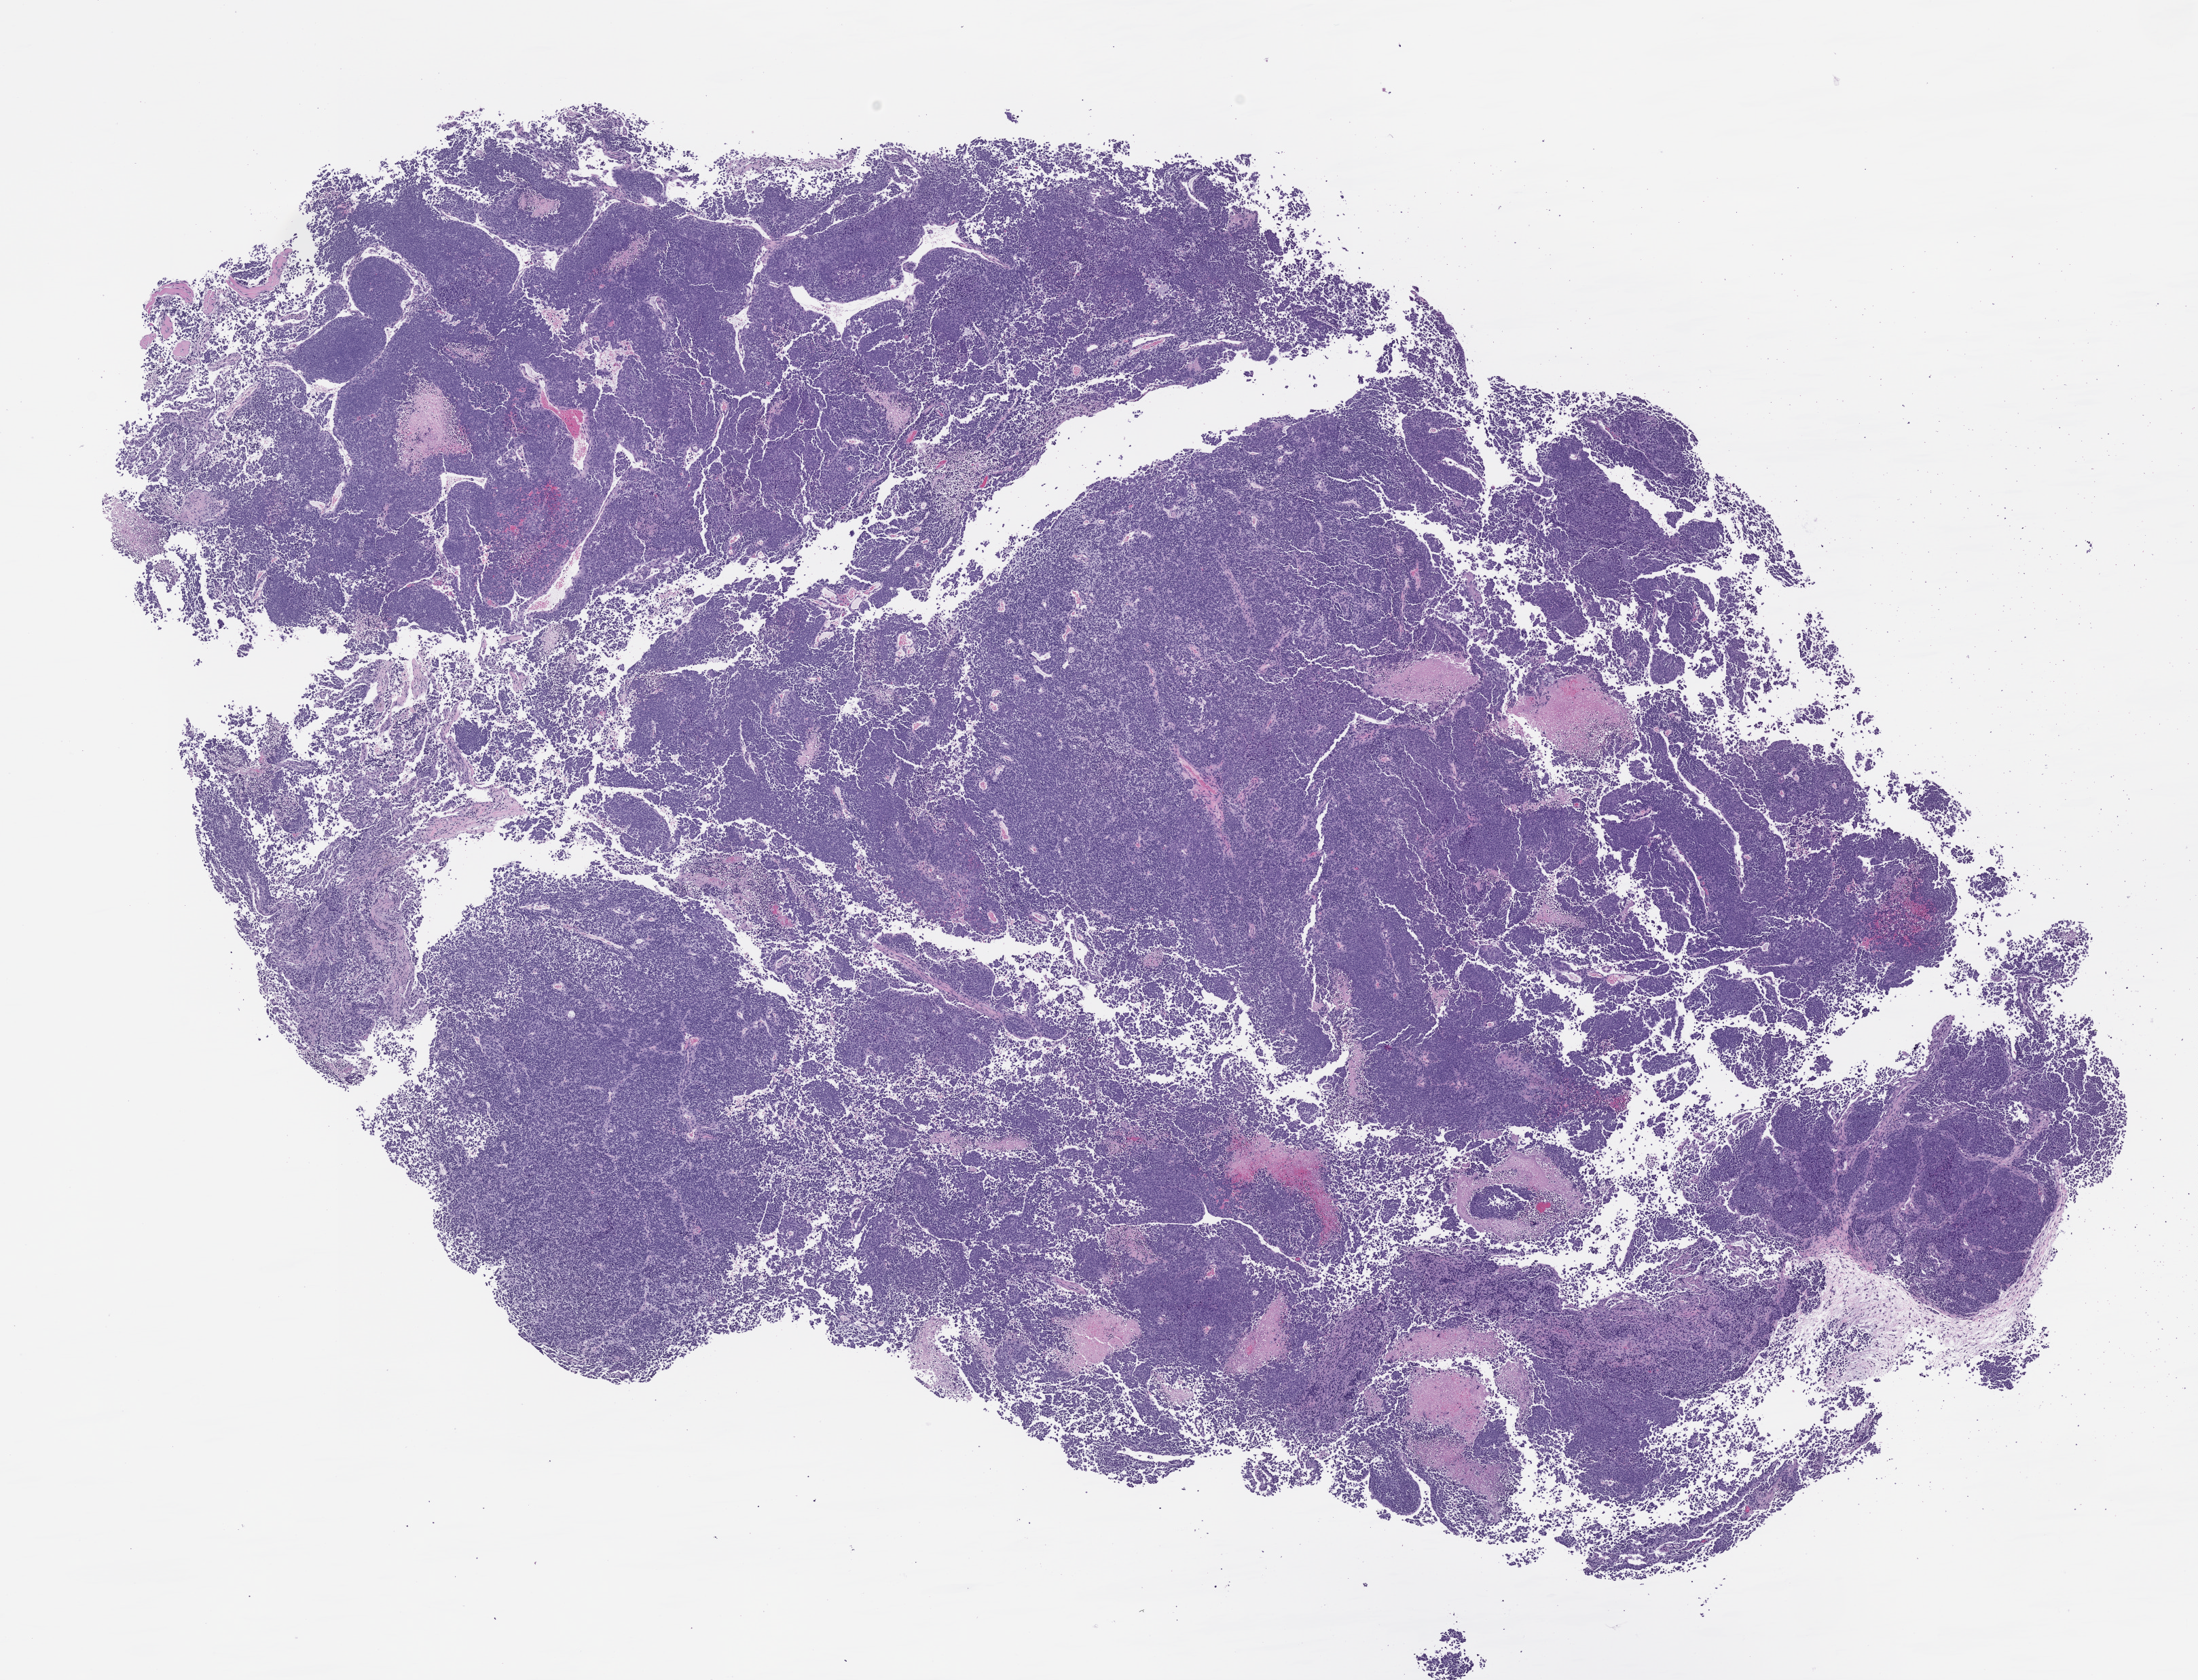
Haematoxylin and eosin whole-slide image of a patient-derived xenograft (PDX) tumor grown in a mouse, passage 0 — whole scanned area (about 13.0 x 9.9 mm) shown as a low-resolution overview. Formalin-fixed, paraffin-embedded (FFPE) tissue. Originating tumor site category: uterus.
- originating patient diagnosis: Carcinosarcoma